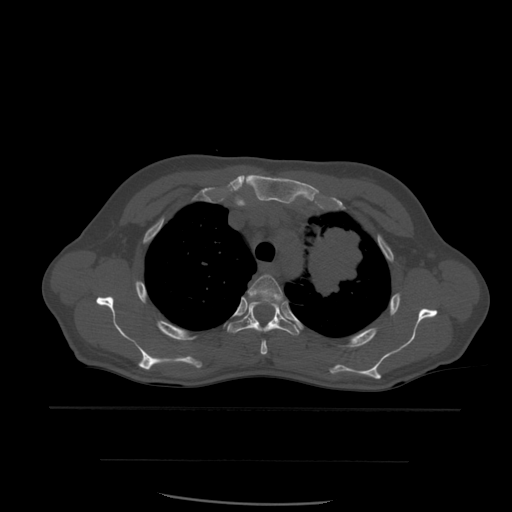
CT including the spine, one axial slice. Slice 432 of 574 in the series (ordered by position). Bone window (W 1800 / L 400 HU). 1.25 mm slice thickness. 512 × 512 image matrix. Patient age 48 years. From the clinical record (not read from this slice): primary cancer: lung; vertebrae with lytic lesions (as recorded): T11.
Structures marked on this image (semi-automatic segmentation, software-assisted and operator-edited):
- T3 vertebra: bounding box [x1, y1, x2, y2] px = [244, 275, 283, 355]
- T4 vertebra: [227, 302, 300, 336]
- T5 vertebra: [276, 299, 284, 303]